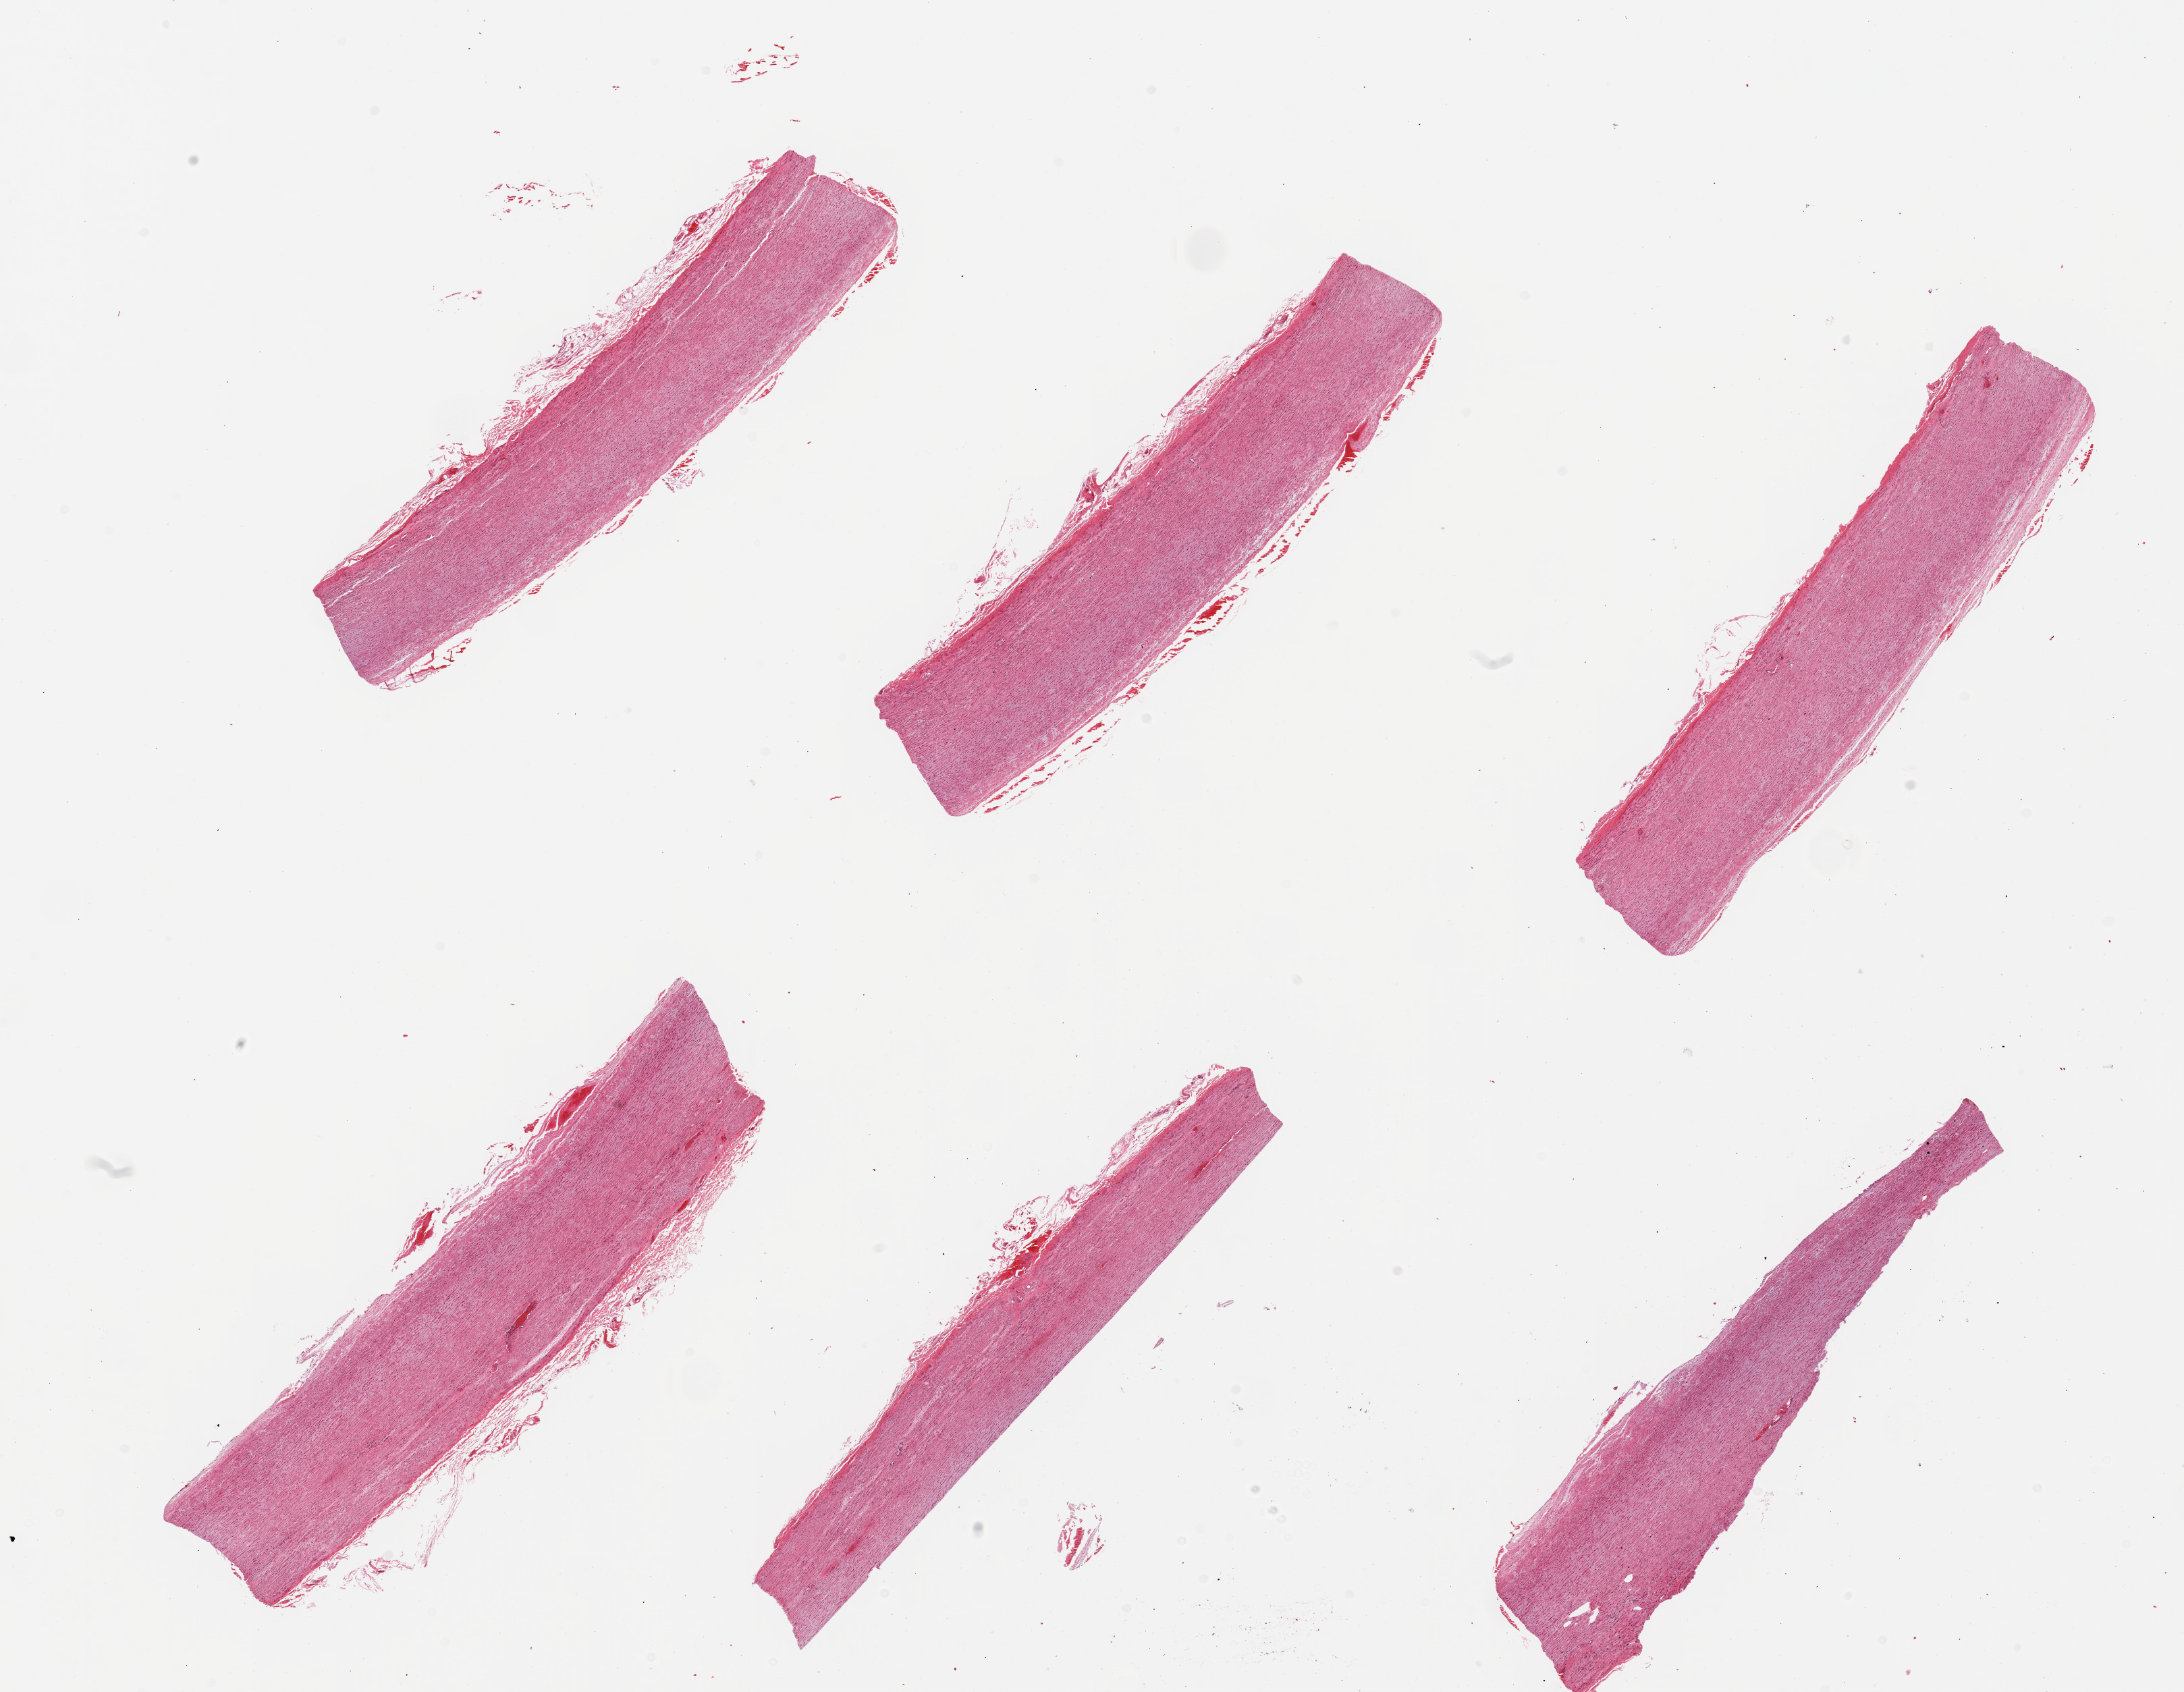
Haematoxylin and eosin whole-slide image, whole scanned area (about 25.6 x 19.8 mm) shown as a low-resolution overview; PAXgene-fixed, paraffin-embedded tissue; sampled site (target tissue): aorta; donor tissue sample.
Review note (as recorded): 6 pieces; well trimmed; early atherosclerotic changes.